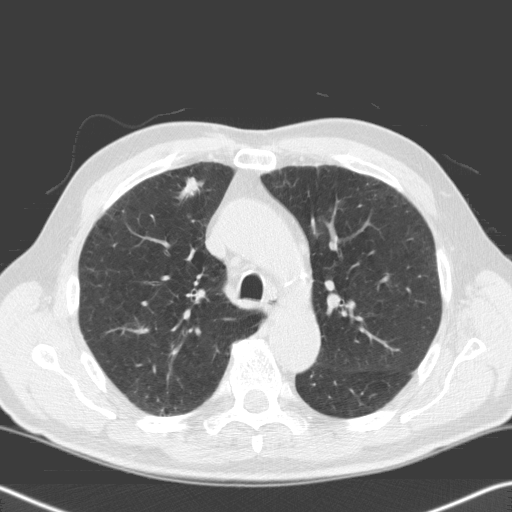
Axial slice from a low-dose chest CT screening exam, baseline annual screen, lung window (W 1500 / L -600 HU), 3.2 mm slice thickness, standard (soft-tissue) reconstruction kernel (C), slice 48 of 170 in the series, 512 × 512 image matrix, field of view 343 × 343 mm. Male, age 68 years at enrolment. Current smoker at enrolment.
Expert reader's lesion annotation, box from (x=164, y=168) to (x=212, y=216) px. Screening reader's record for this exam (one nodule recorded; not confirmed to be the boxed lesion): non-calcified nodule or mass ≥4 mm, right upper lobe, 18 × 12 mm, spiculated (stellate) margins, soft tissue attenuation. Later outcome: lung cancer diagnosed 73 days after this screen — squamous cell carcinoma, NOS, right upper lobe, moderately differentiated (G2), stage IIIA (AJCC 6th edition), 7 mm at pathology.